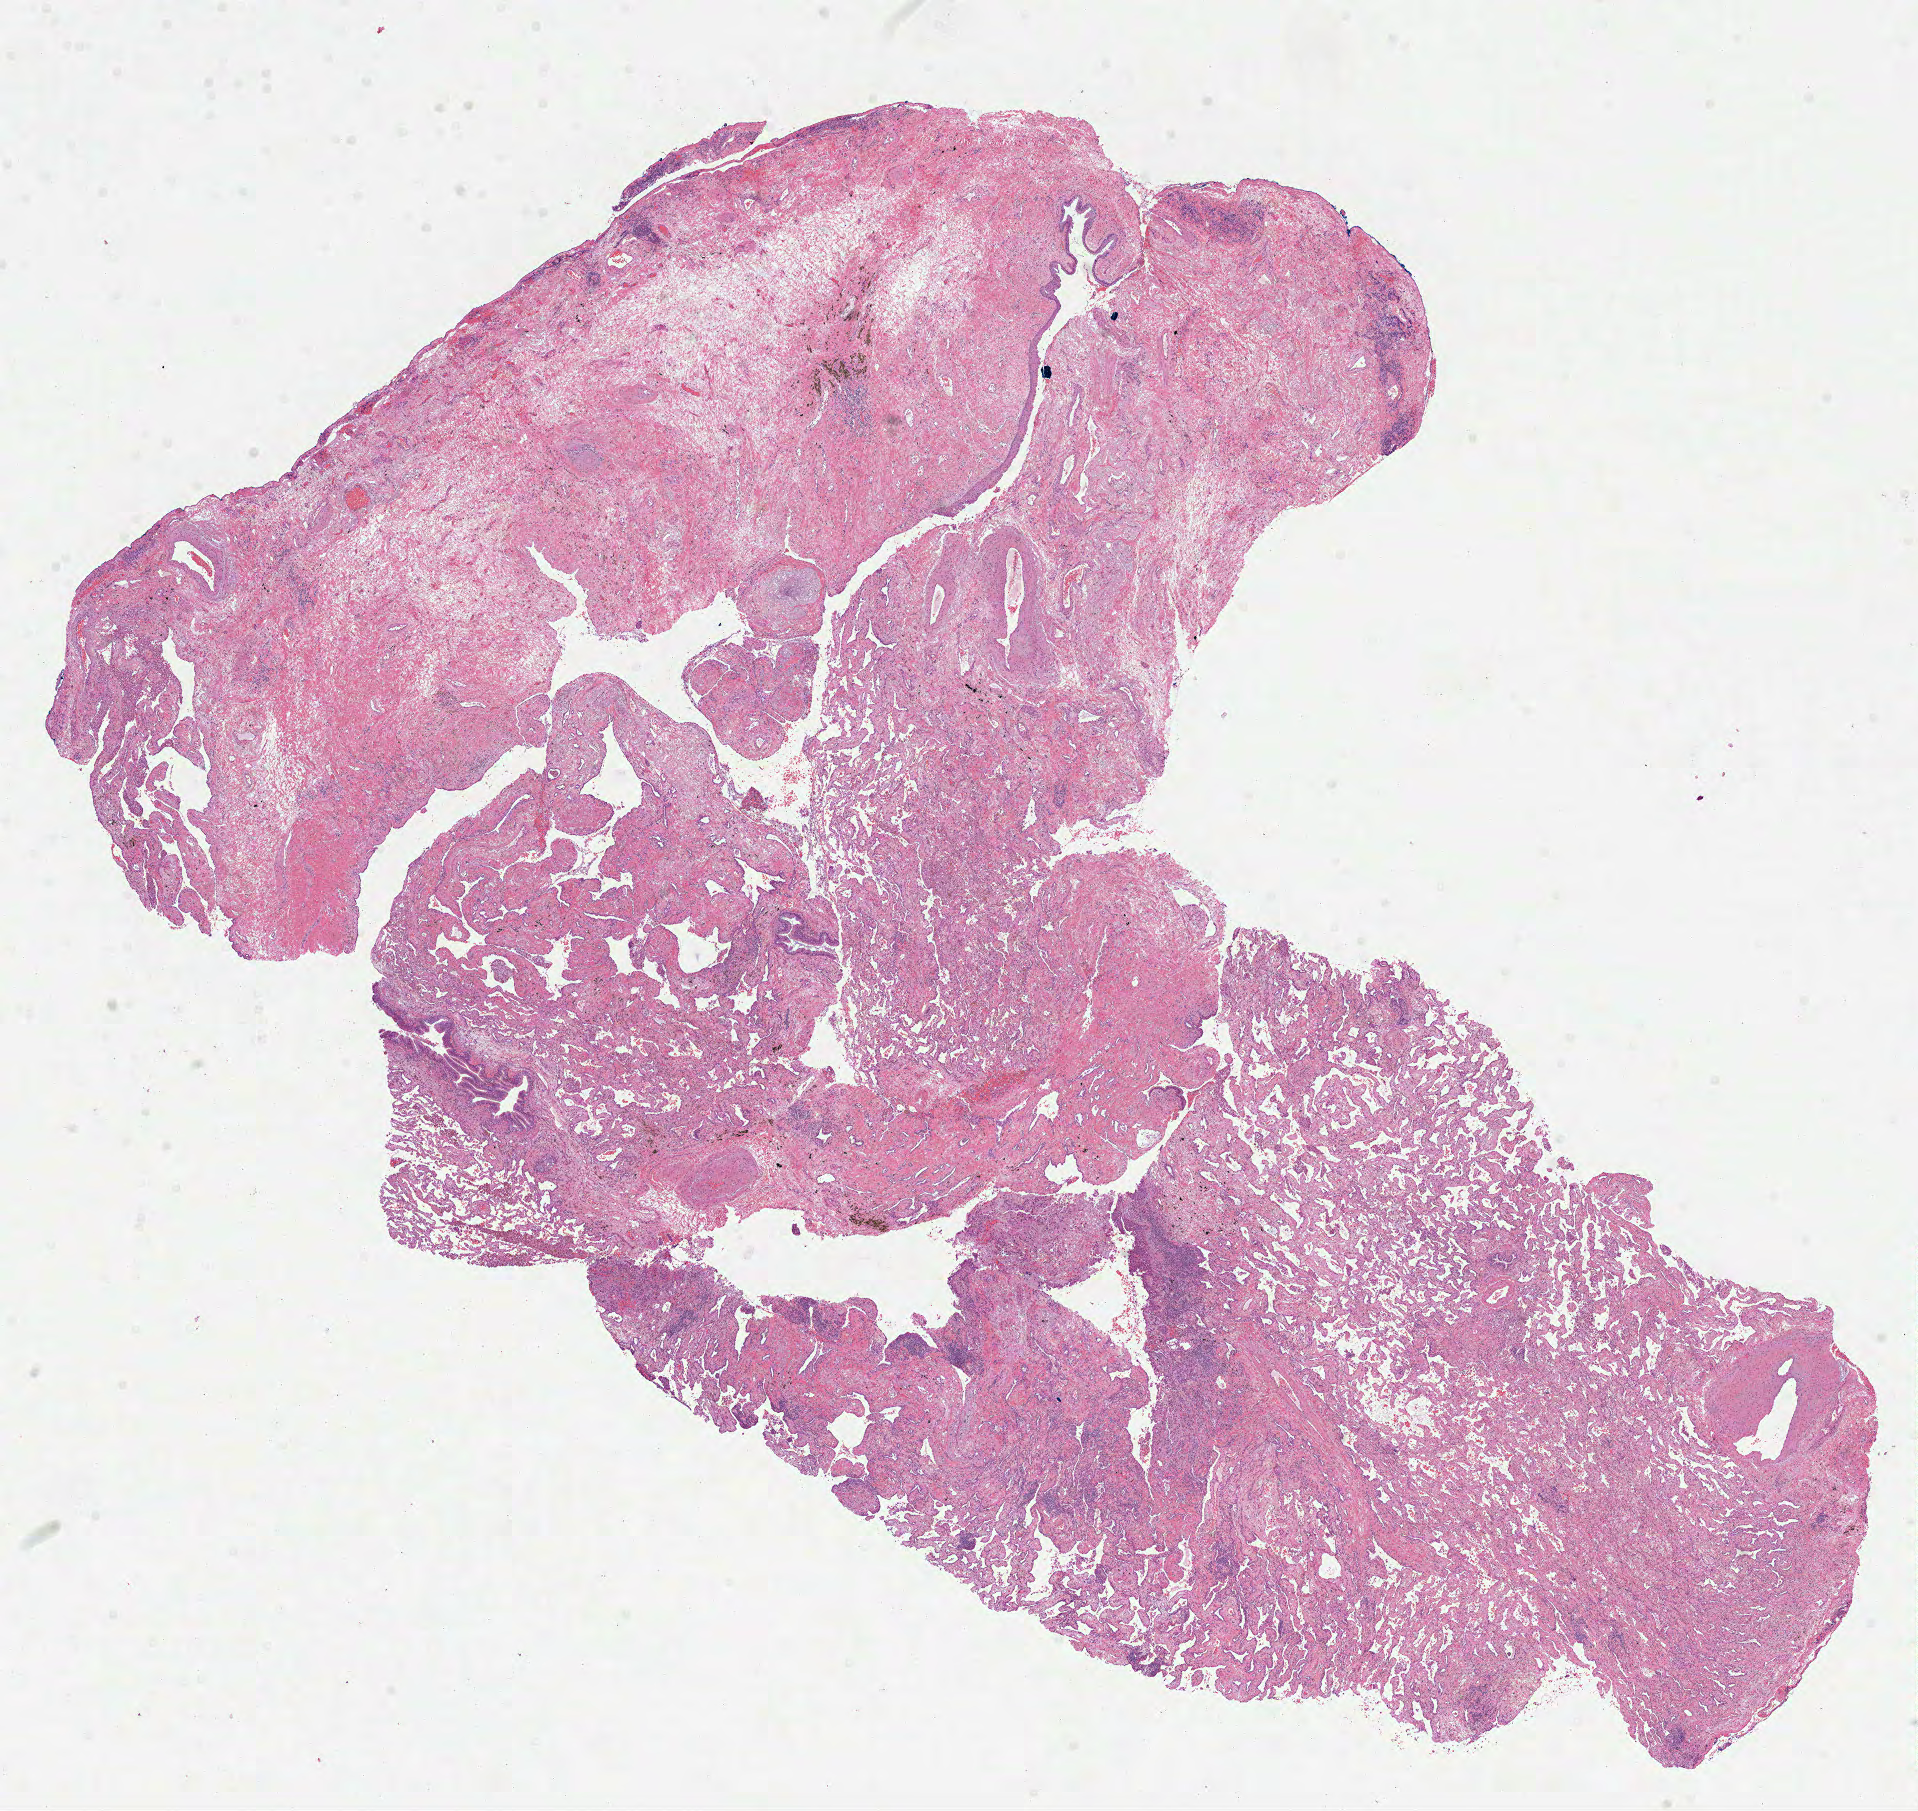
Whole-slide histology image, H&E — whole scanned area (about 15.5 x 14.6 mm, from a 40x scan) shown as a low-resolution overview; FFPE section; lung, primary tumour sample. Male patient; age at initial diagnosis 60 years.
AJCC pathologic stage: IB (7th edition). Histologic diagnosis: Squamous cell carcinoma, NOS (upper lobe, lung).